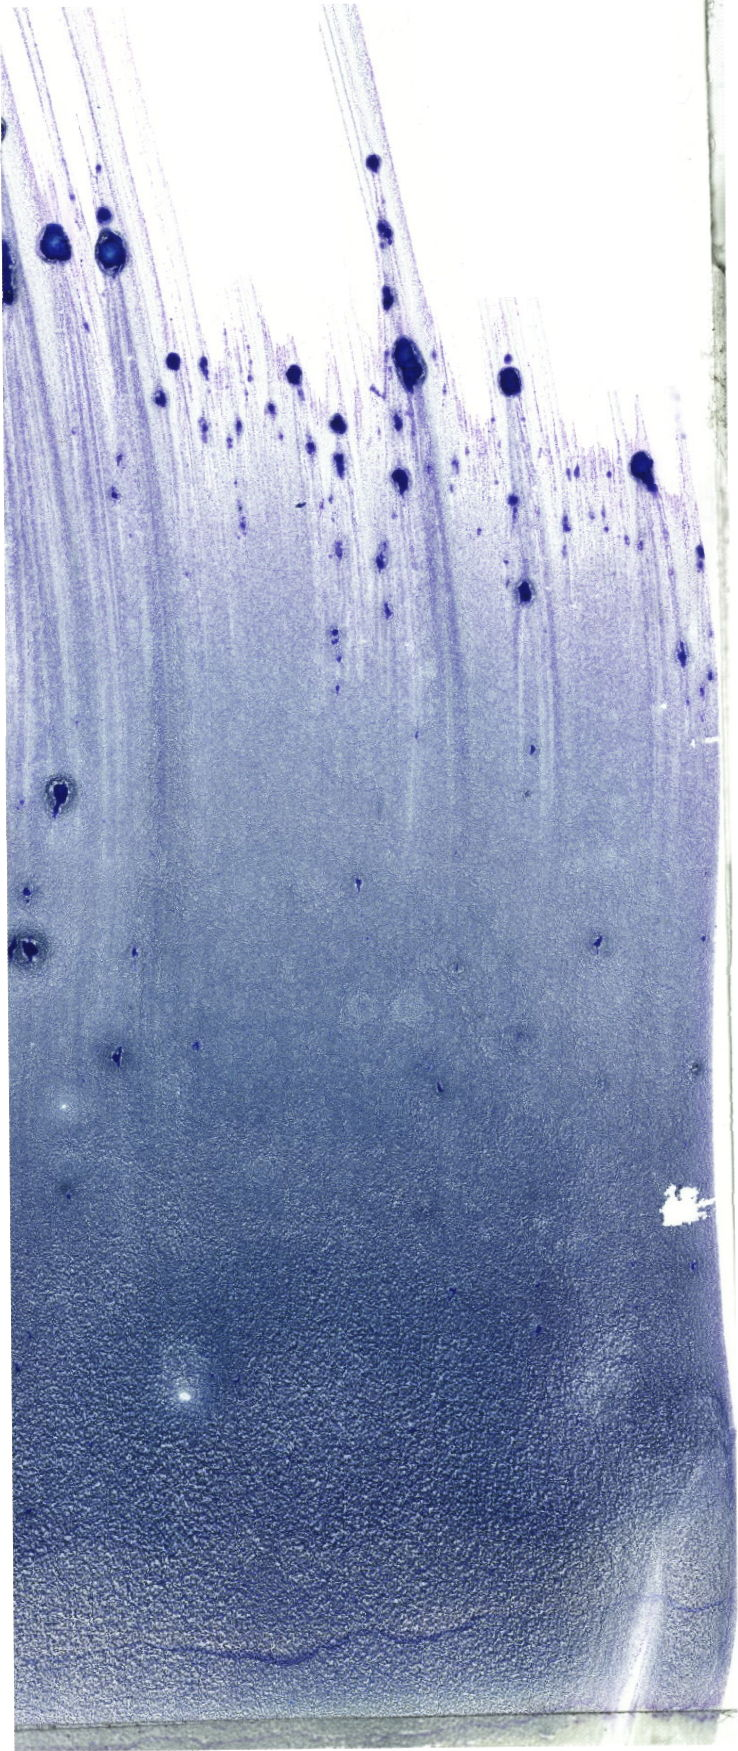
Bone marrow aspirate smear, May-Grünwald–Giemsa stain, whole-slide image — whole scanned area (about 20.9 x 49.6 mm) shown as a low-resolution overview. Female patient.
Diagnosis: Acute Myeloid Leukemia with Maturation.